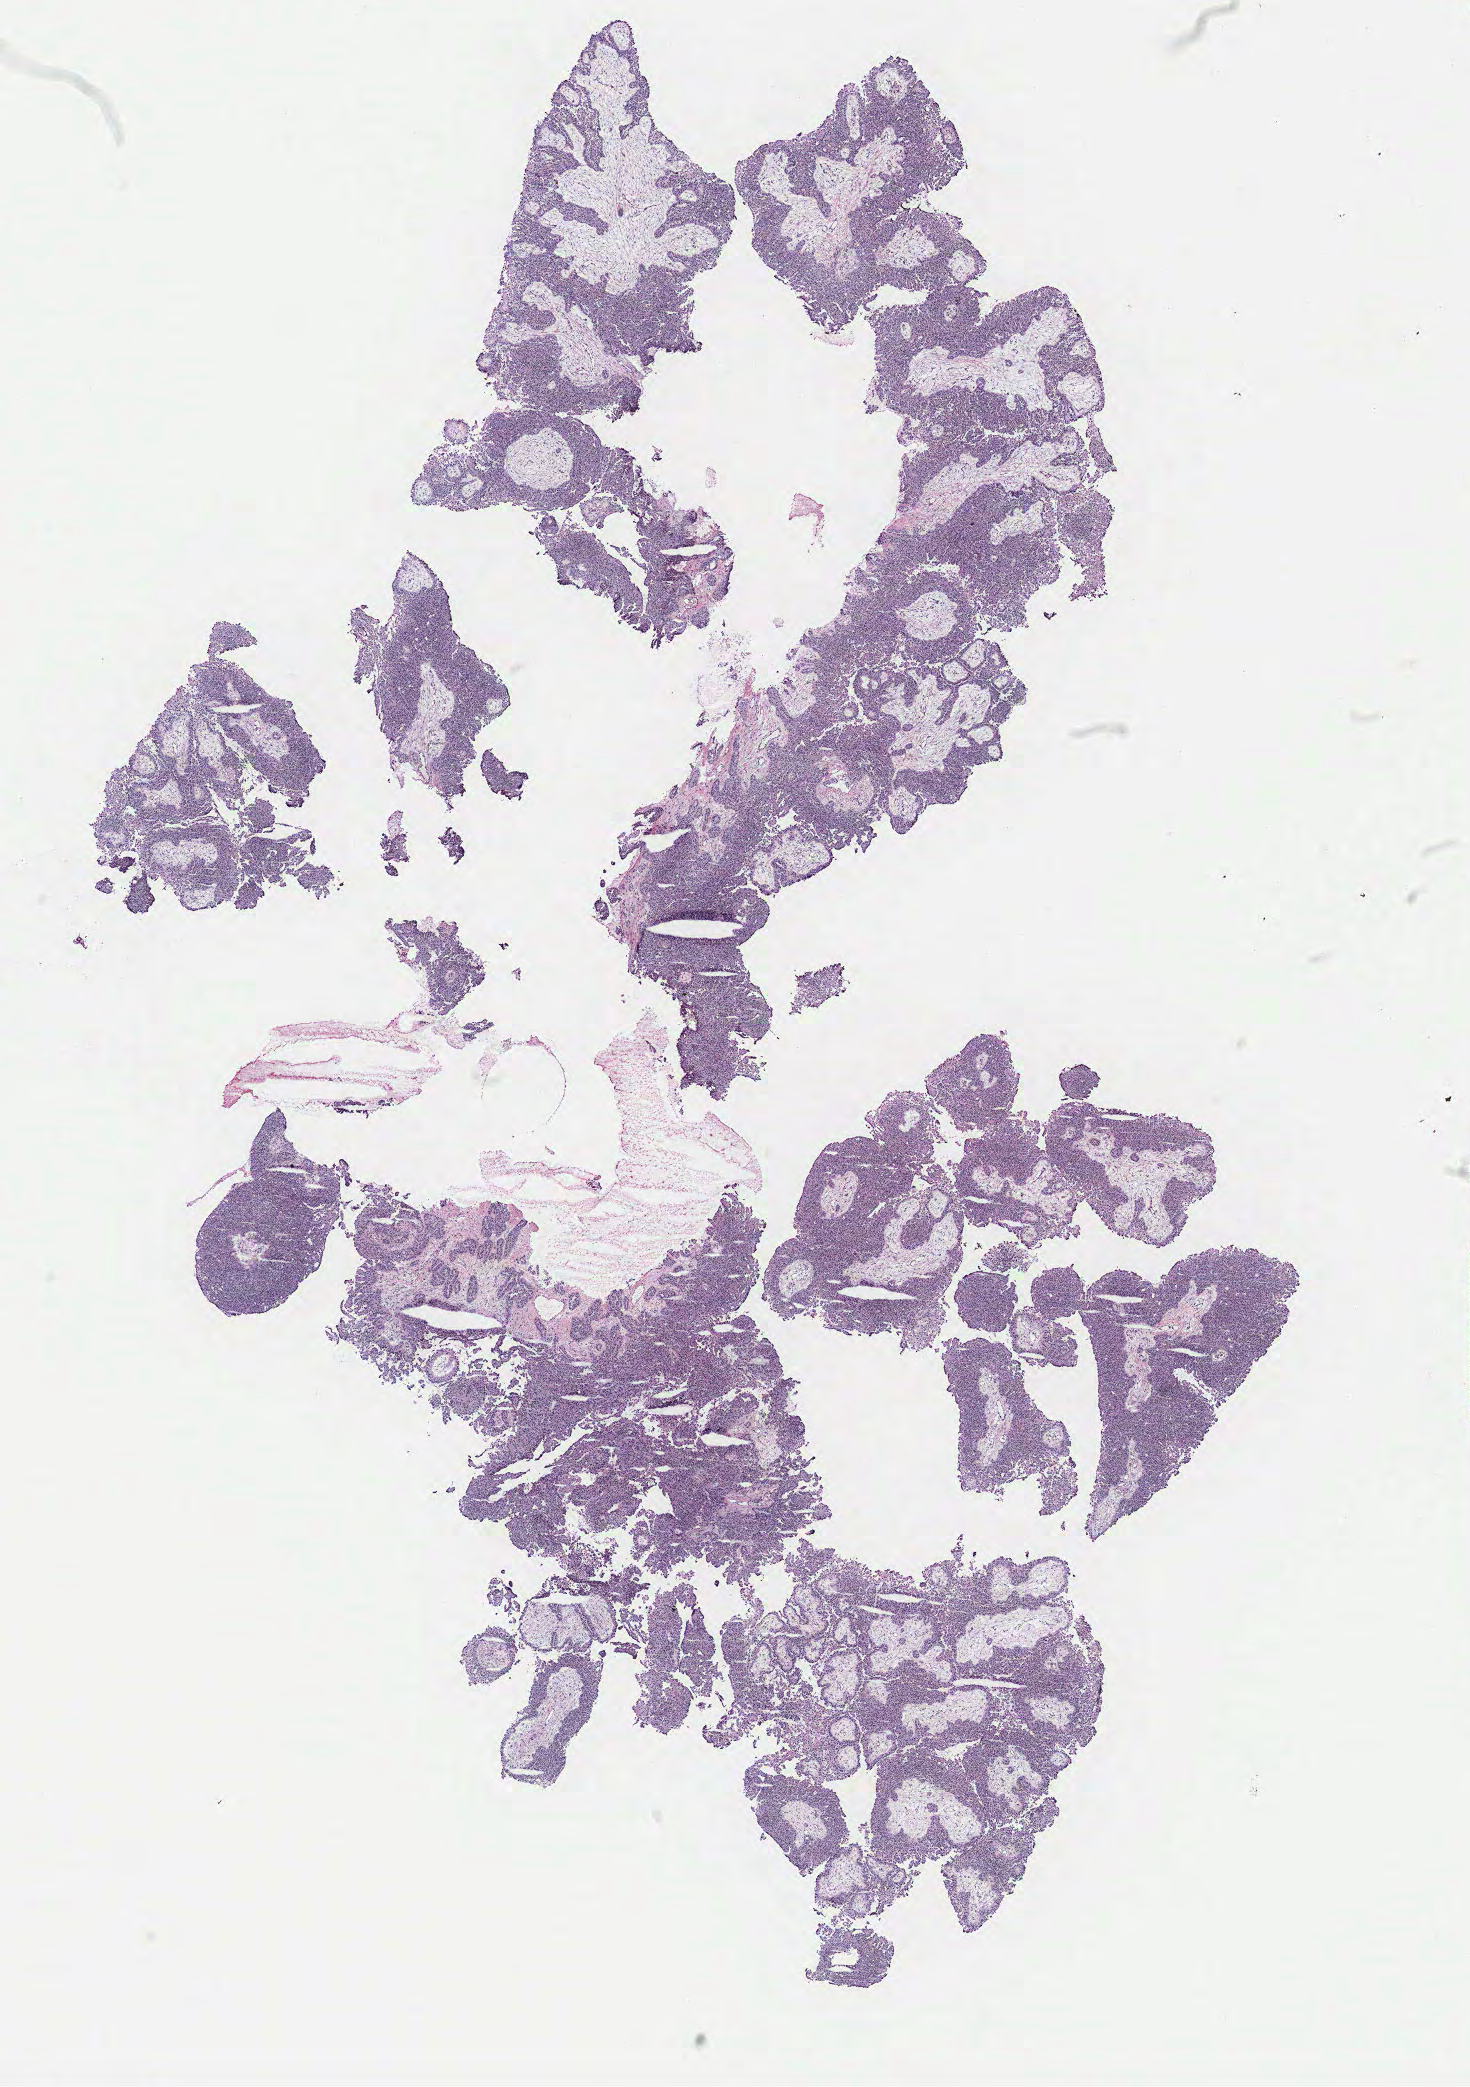
Whole-slide histology image, Hematoxylin and eosin (H&E) stained, a low-resolution overview of the entire scanned area, about 11.8 x 16.7 mm (slide scanned at 40x), tumour tissue sample, ovary. Female, 85 y/o.
Histologic diagnosis: Serous adenocarcinoma, NOS (fallopian tube).